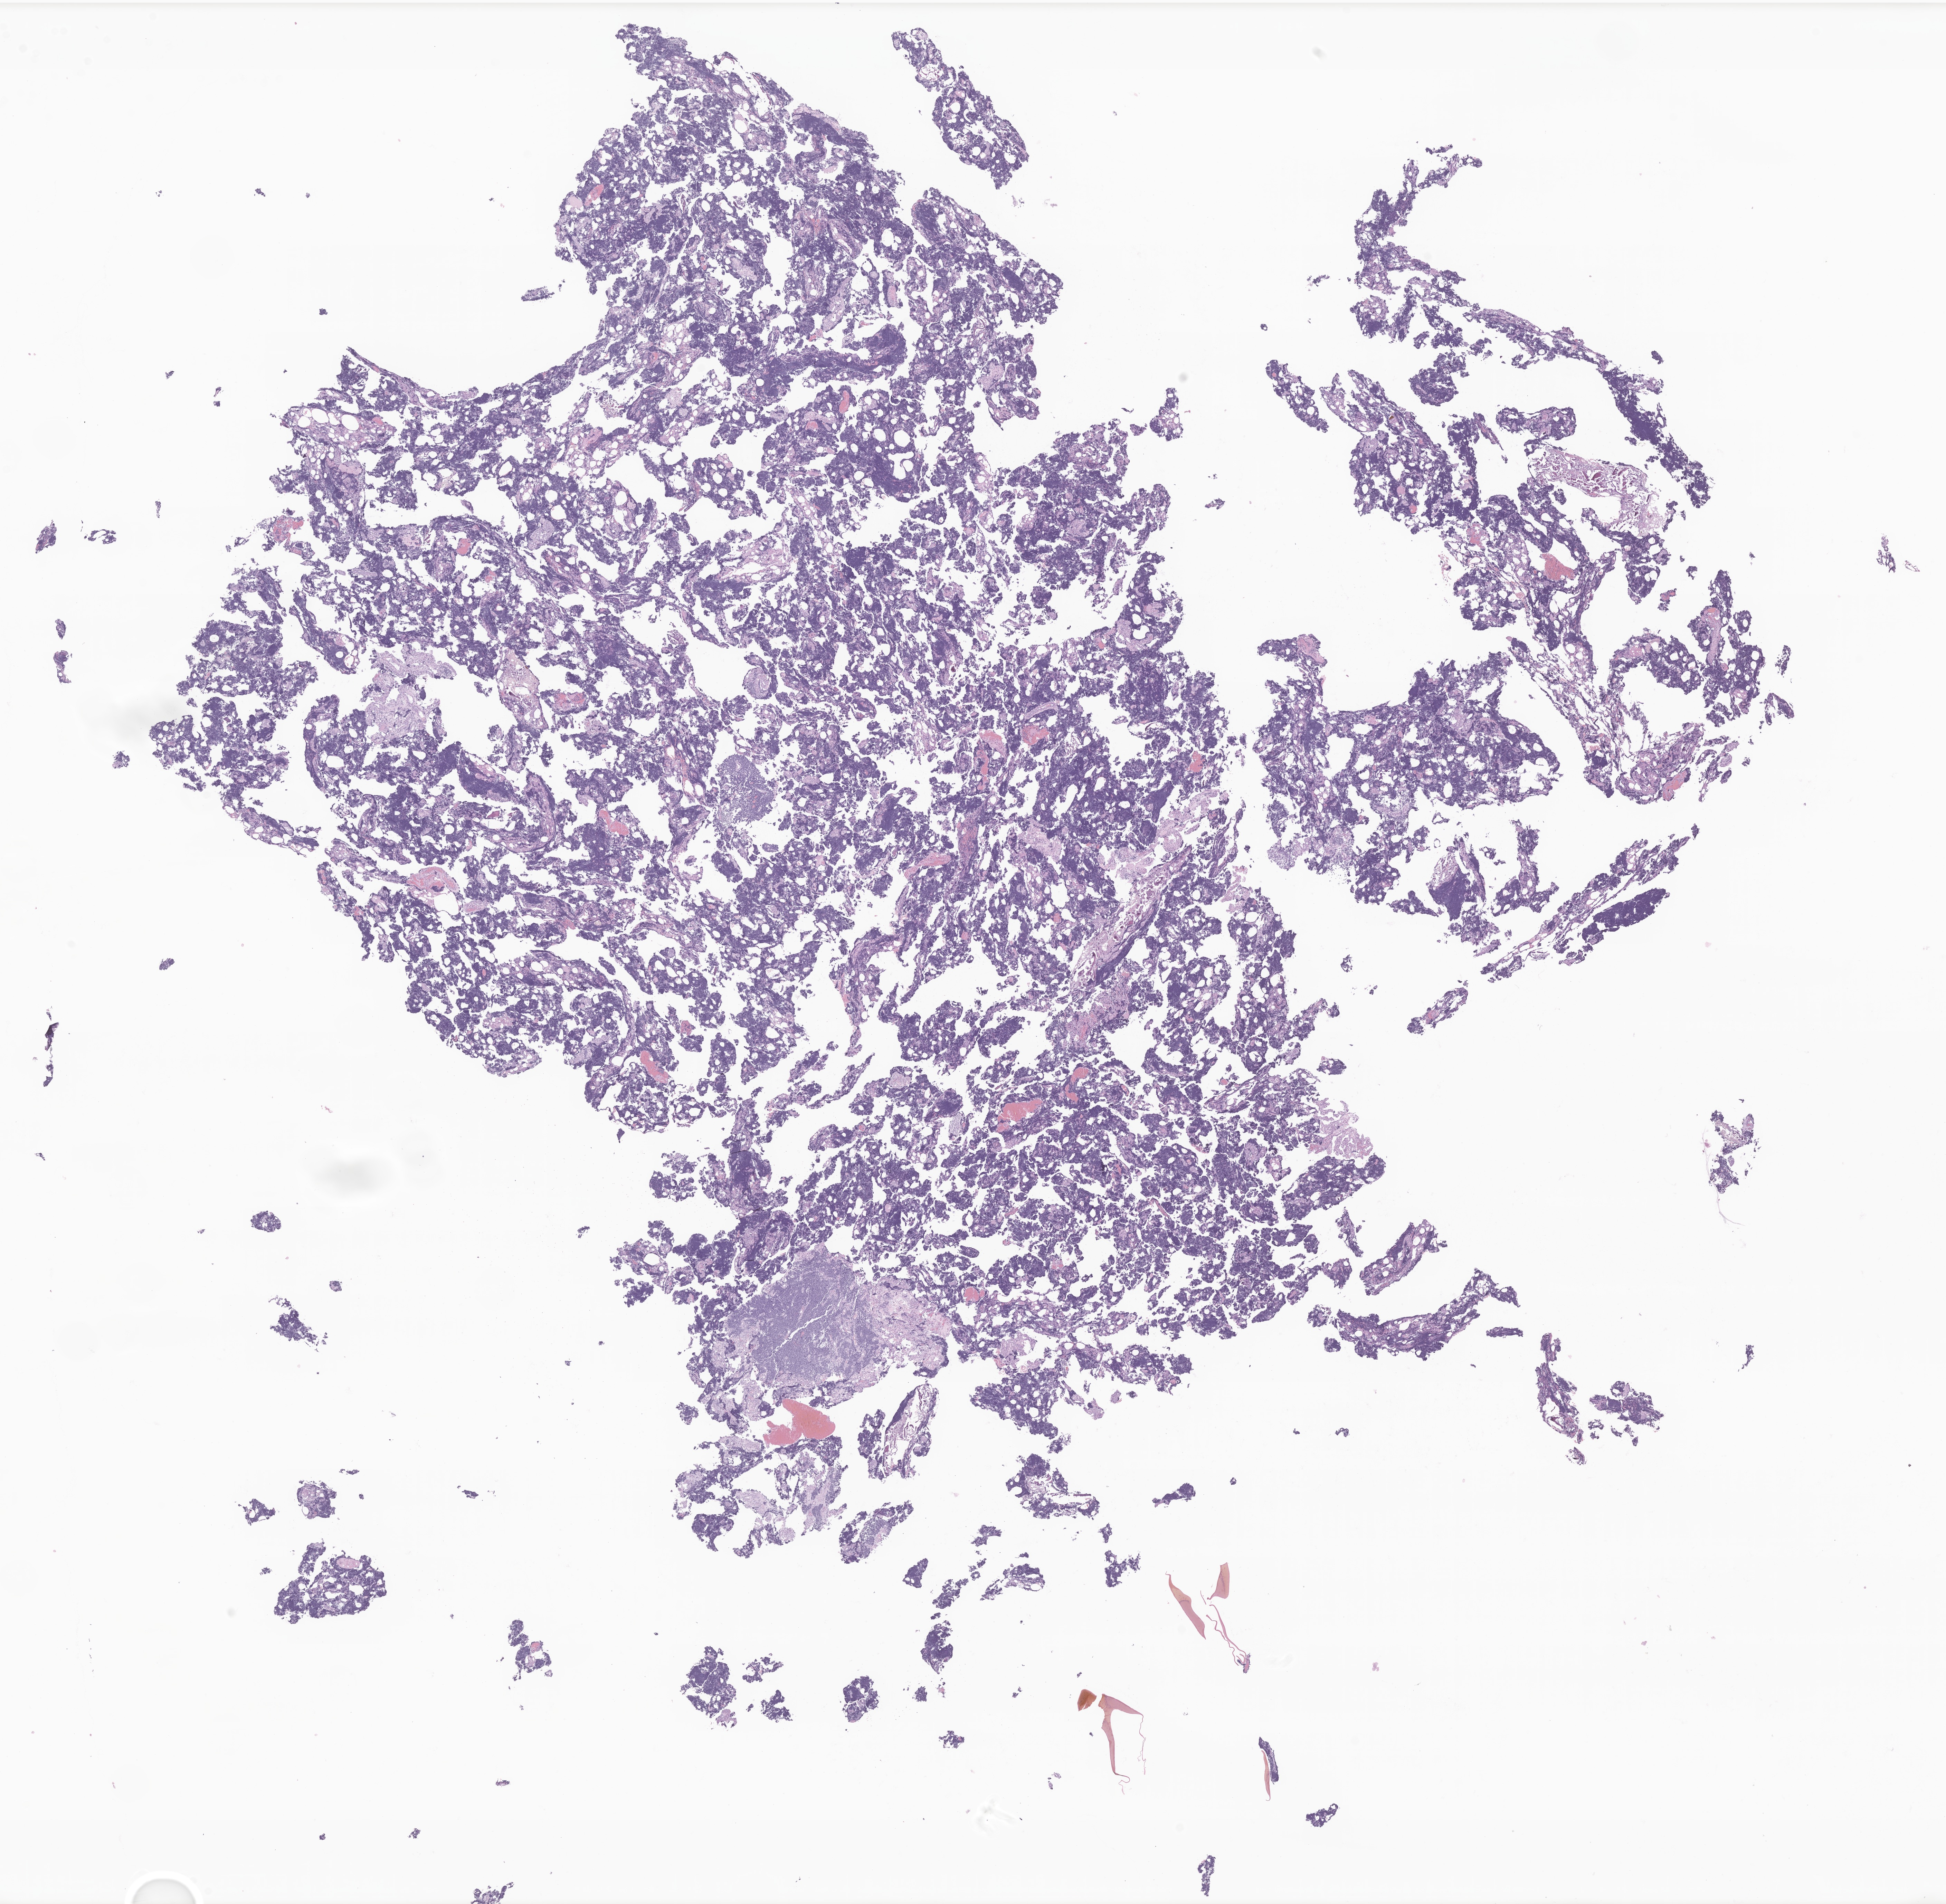
Hematoxylin and eosin (H&E) whole-slide image of tumor tissue from the brain, whole scanned area (about 23.7 x 23.2 mm) shown as a low-resolution overview, FFPE section. Patient: male, age 69 months (5 years 9 months).
Recorded diagnosis: Medulloblastoma, NOS.